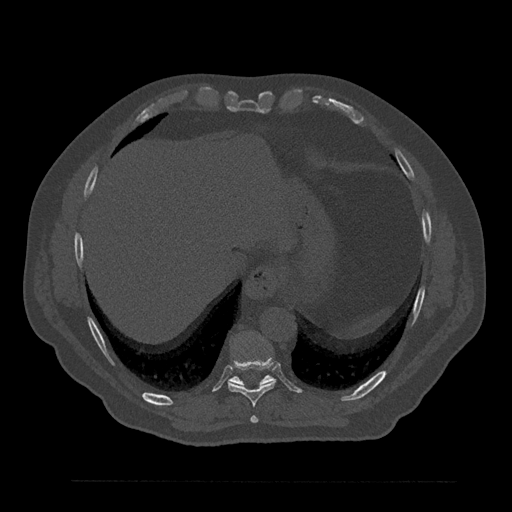
CT including the spine, one axial slice; position 388 of 797 along the scan axis; bone window (W 1800 / L 400 HU); 0.5 mm slice thickness; 512 × 512 image matrix, field of view 430 × 430 mm. Patient: male, 61 years. From the clinical record (not read from this slice): primary cancer: prostate.
Outlined on this slice (semi-automatically segmented with operator editing):
- T10 vertebra: bounding box (x1, y1, x2, y2) in pixels: (228, 375, 274, 386)
- T8 vertebra: (250, 416, 258, 423)
- T9 vertebra: (228, 357, 275, 407)